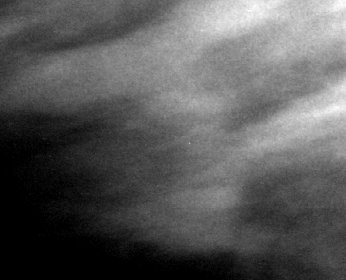
Cropped region of a digitized screen-film mammogram centred on a radiologist-marked abnormality; right breast; MLO view; BI-RADS breast density category 1 (scale 1–4).
- Finding: mass, shape lobulated, margins obscured; BI-RADS assessment category 3; pathology result (as recorded, not read from the image): benign.